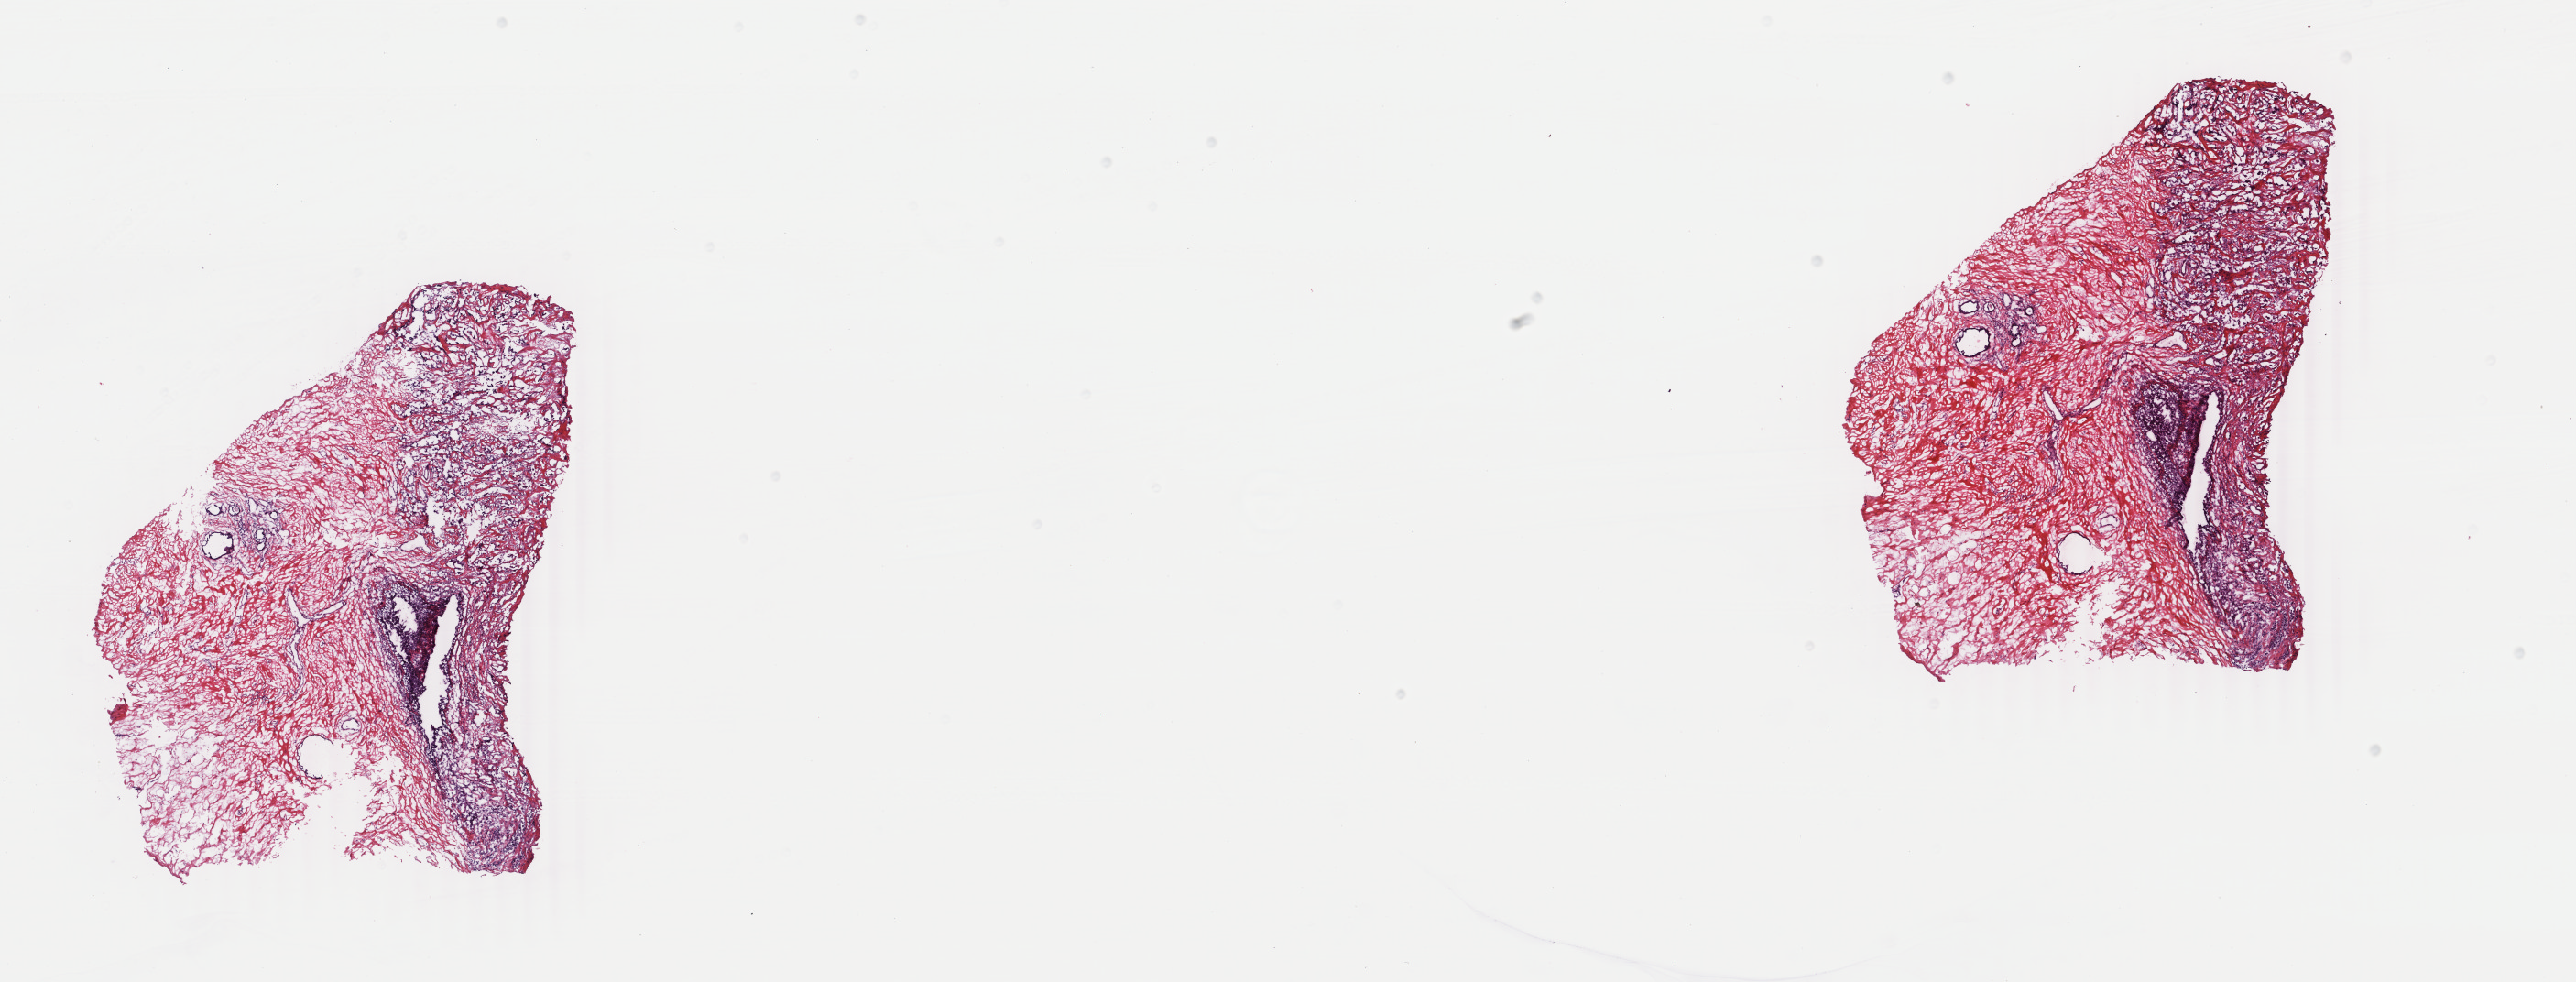
Digitized H&E tissue section (whole slide), whole scanned area (about 22.4 x 8.5 mm, from a 40x scan) shown as a low-resolution overview. Frozen section. Sample: primary tumour, breast. Female, age 63 years at initial diagnosis. Composition of this section per pathologist review: tumour cells 65%, tumour nuclei 65%, normal cells 4%, stromal cells 30%, necrosis 1%. Inflammatory infiltration, as recorded: lymphocyte infiltration 3%, monocyte infiltration 0%, neutrophil infiltration 0%.
- AJCC pathologic stage: IIIB (4th edition)
- histologic diagnosis: Infiltrating duct carcinoma, NOS